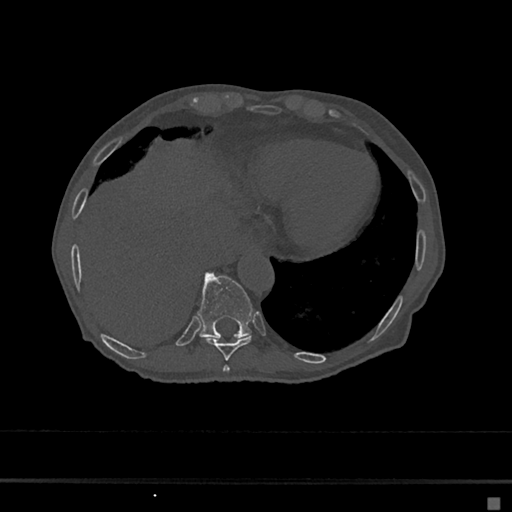
CT including the spine, one axial slice. Slice 249 of 797 in the series (ordered by position). Bone window (W 1800 / L 400 HU). 0.5 mm slice thickness. 512 × 512 image matrix, field of view 360 × 360 mm. Female patient, age 68 years. Case-level facts recorded for this patient, not image findings: primary cancer: renal.
Annotated regions visible in this slice (semi-automatically segmented with operator editing):
- T10 vertebra: bounding box (x1, y1, x2, y2) in pixels: (197, 273, 253, 339)
- T8 vertebra: (223, 366, 230, 373)
- T9 vertebra: (203, 336, 252, 361)